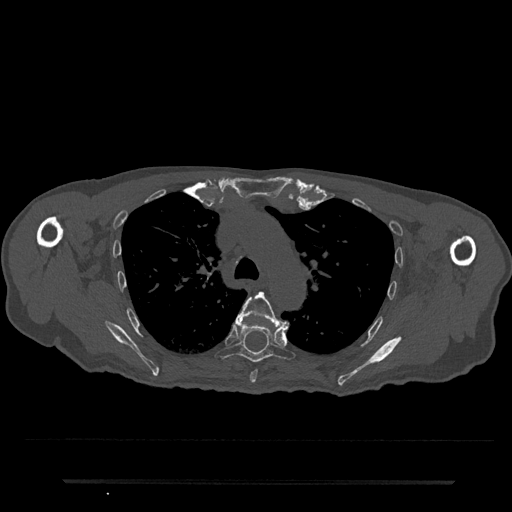
CT including the spine, one axial slice. 120 kVp. Bone window (W 1800 / L 400 HU). 512 × 512 image matrix. Male patient, age 74 years. Case-level facts recorded for this patient, not image findings: primary cancer: prostate.
Structures marked on this image (semi-automatic segmentation, software-assisted and operator-edited):
- T5 vertebra: bounding box <236,292,289,383> (left, top, right, bottom; pixels)
- T6 vertebra: <216,317,295,363>